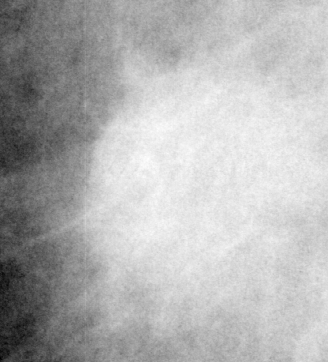
Crop from a digitized film mammogram around one marked abnormality, right breast, MLO view.
Marked abnormality: mass, shape round, margins spiculated; BI-RADS assessment category 5; subtlety rating 5 on a 1 (subtle) to 5 (obvious) scale; pathology result (as recorded, not read from the image): malignant.